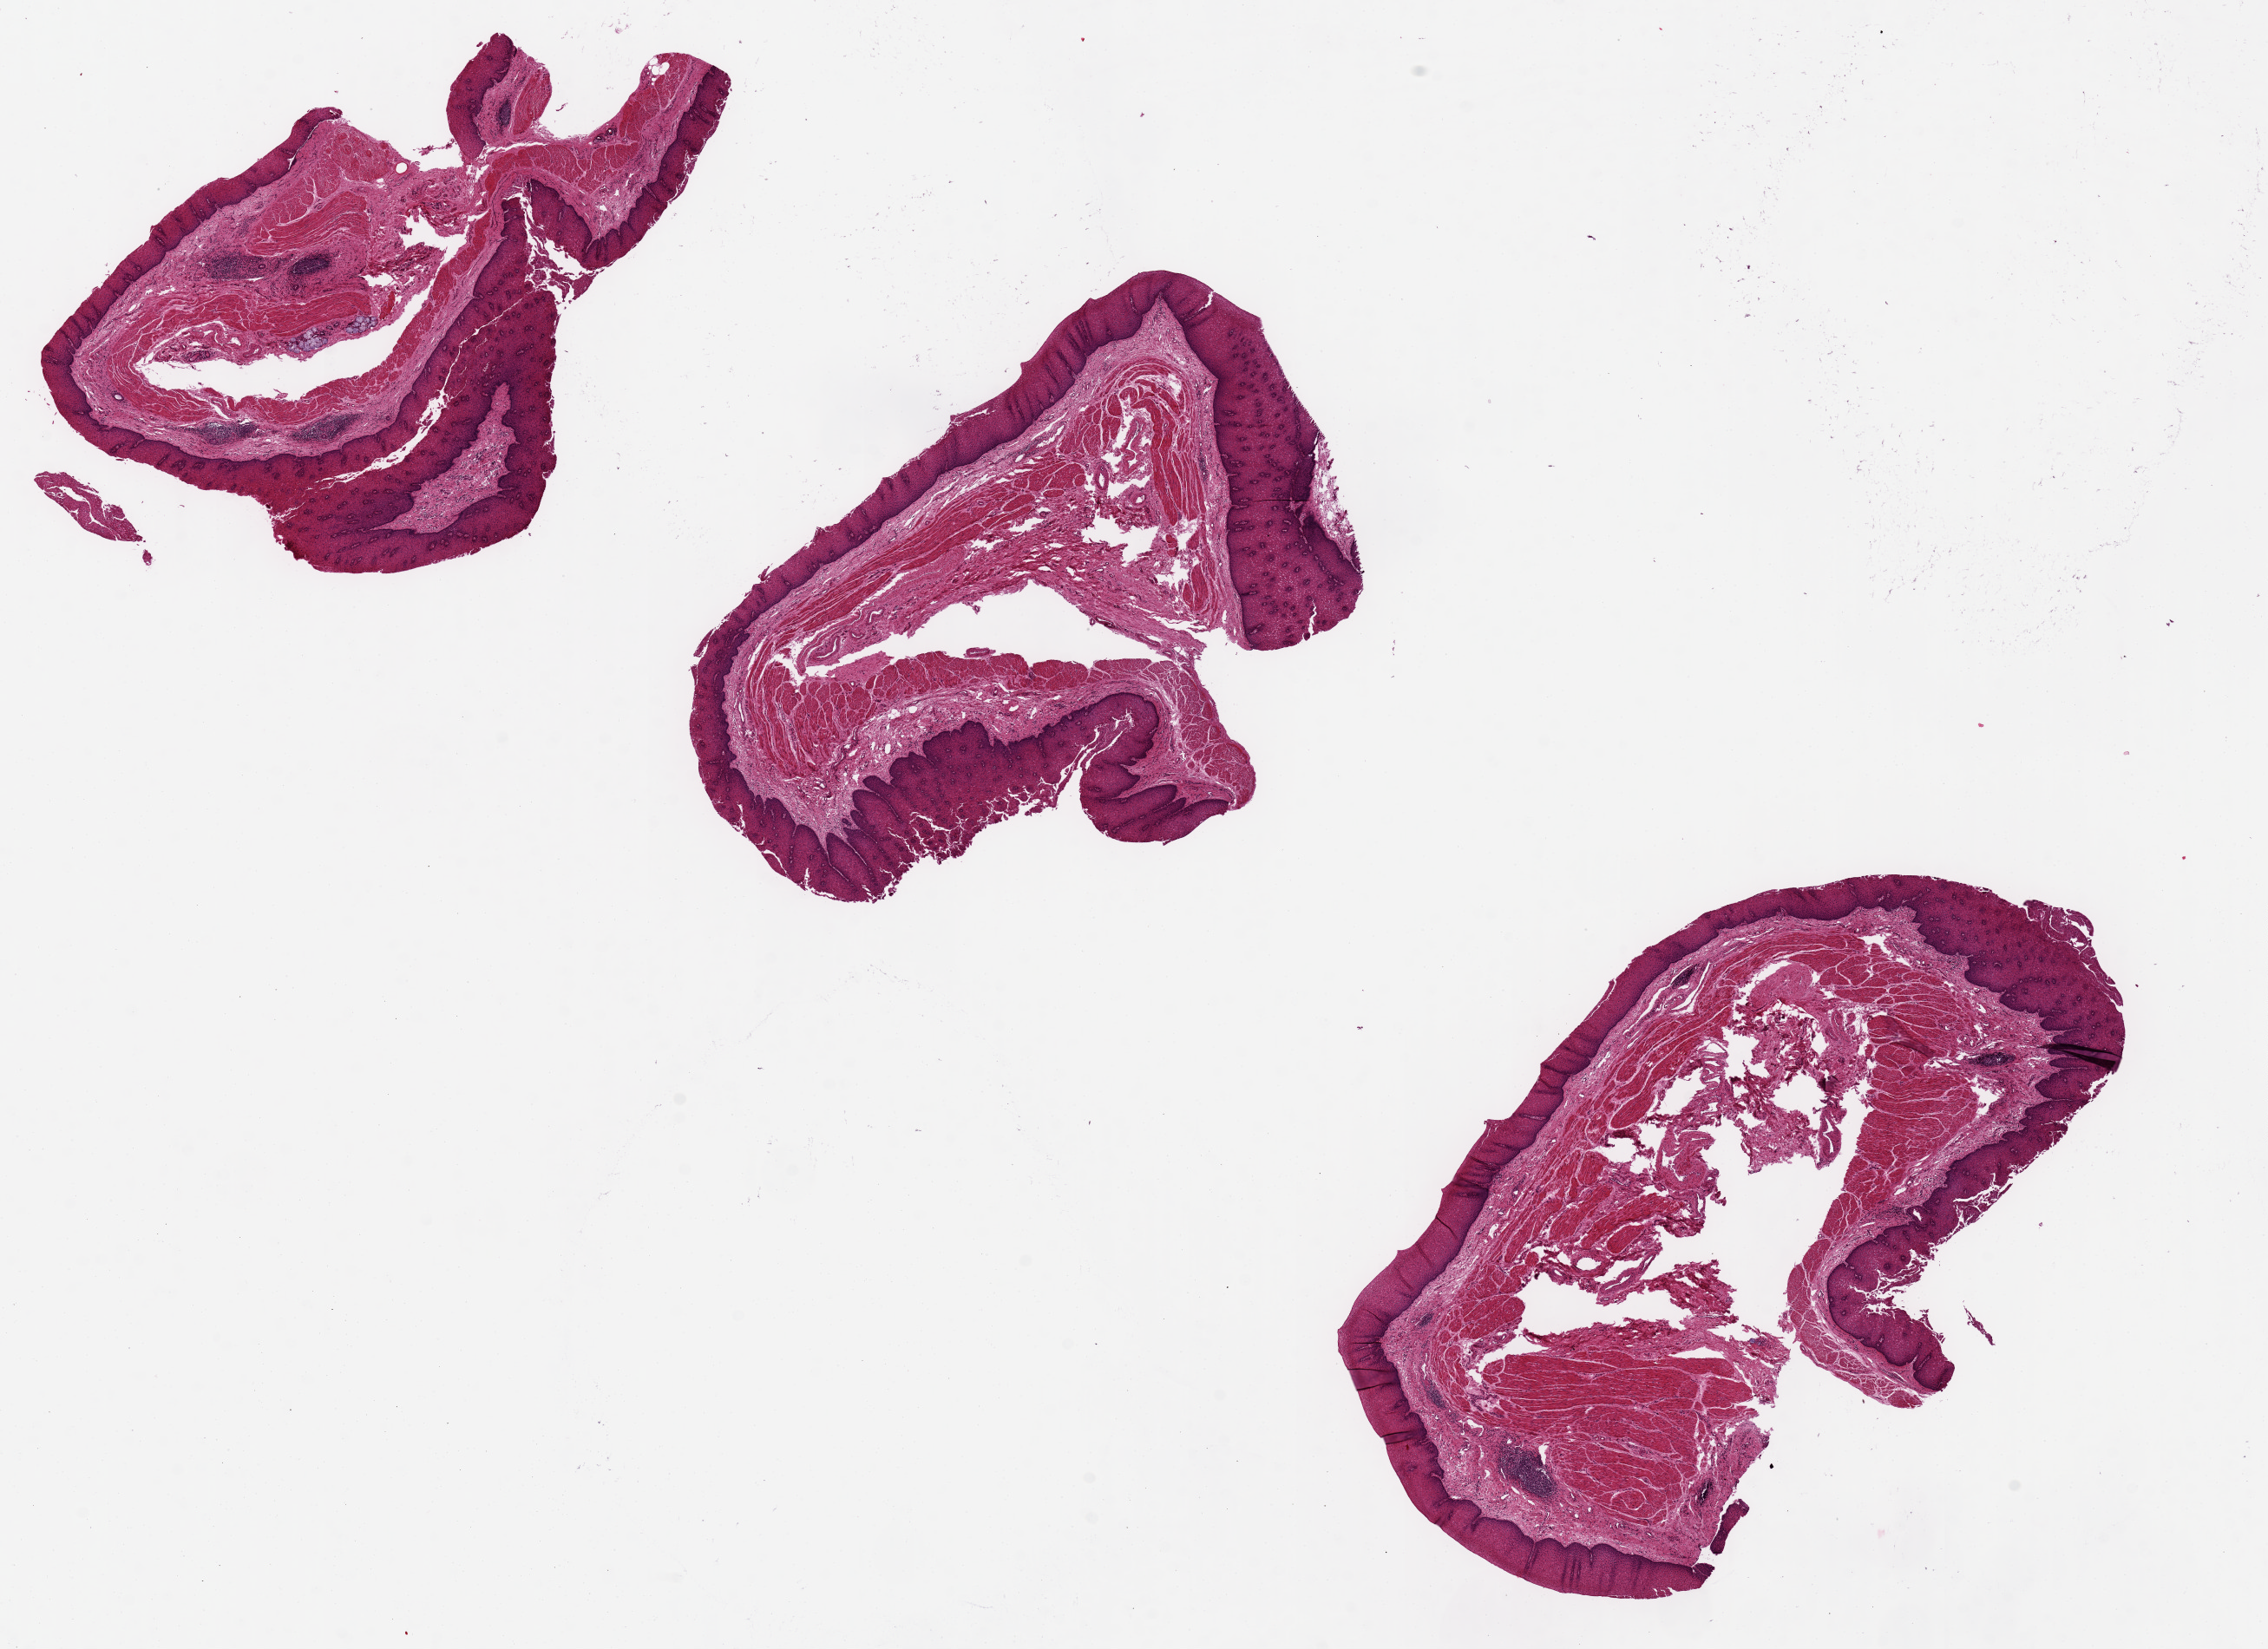
Digitized H&E-stained section, low-resolution overview of the scanned area, about 20.7 x 15.0 mm (slide scanned at 20x). PAXgene-fixed, paraffin-embedded tissue. Sampled site (target tissue): esophageal mucous membrane. Tissue donor sample. Donor: male.
Review note (as recorded): OK for analysis.